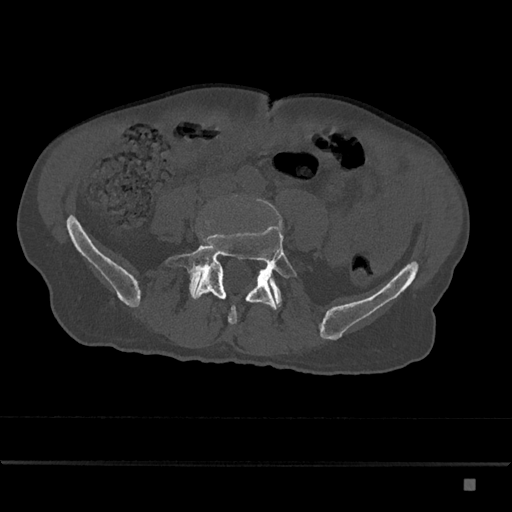
CT including the spine, one axial slice. Slice 283 of 797 in the series (ordered by position). Bone window (W 1800 / L 400 HU). 0.5 mm slice thickness. 512 × 512 image matrix, field of view 390 × 390 mm. Patient: male, 72 years. From the clinical record (not read from this slice): primary cancer: prostate.
Structures marked on this image (semi-automatic segmentation, software-assisted and operator-edited):
- L5 vertebra: bounding box <167,223,297,324> (left, top, right, bottom; pixels)